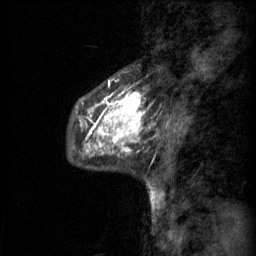
Breast MRI (dynamic contrast-enhanced), one sagittal slice; slice 20 of 60 in the series (ordered by position); 3 images stored at this slice position (order not interpretable as contrast timing); 1.5 T; TE 4.2 ms, TR 11 ms; 2 mm slice thickness; 256 × 256 image matrix, field of view 200 × 200 mm. Patient: female, 48 years.
Annotated regions visible in this slice (semi-automatically segmented with operator editing):
- analysis volume of interest (the breast-tissue region the enhancement analysis was run in; not a lesion): bounding box [x1, y1, x2, y2] px = [77, 78, 146, 147]
- tumour enhancement mask (voxels above the 70 % enhancement threshold inside the analysis volume of interest): [89, 80, 145, 147]